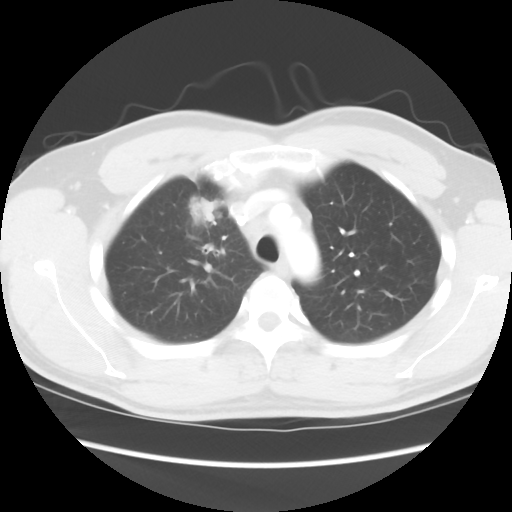
Chest CT, one axial slice. Position 67 of 80 along the scan axis. 120 kVp. Lung window (W 1500 / L -600 HU). 512 × 512 image matrix. Patient: male, 35 years. Case-level facts recorded for this patient, not image findings: clinical TNM (as recorded): T1c N1 M1b.
Annotated regions visible in this slice (rectangle marked by the reading radiologist):
- lung tumour (recorded histology: adenocarcinoma): bounding box <201,195,219,227> (left, top, right, bottom; pixels)